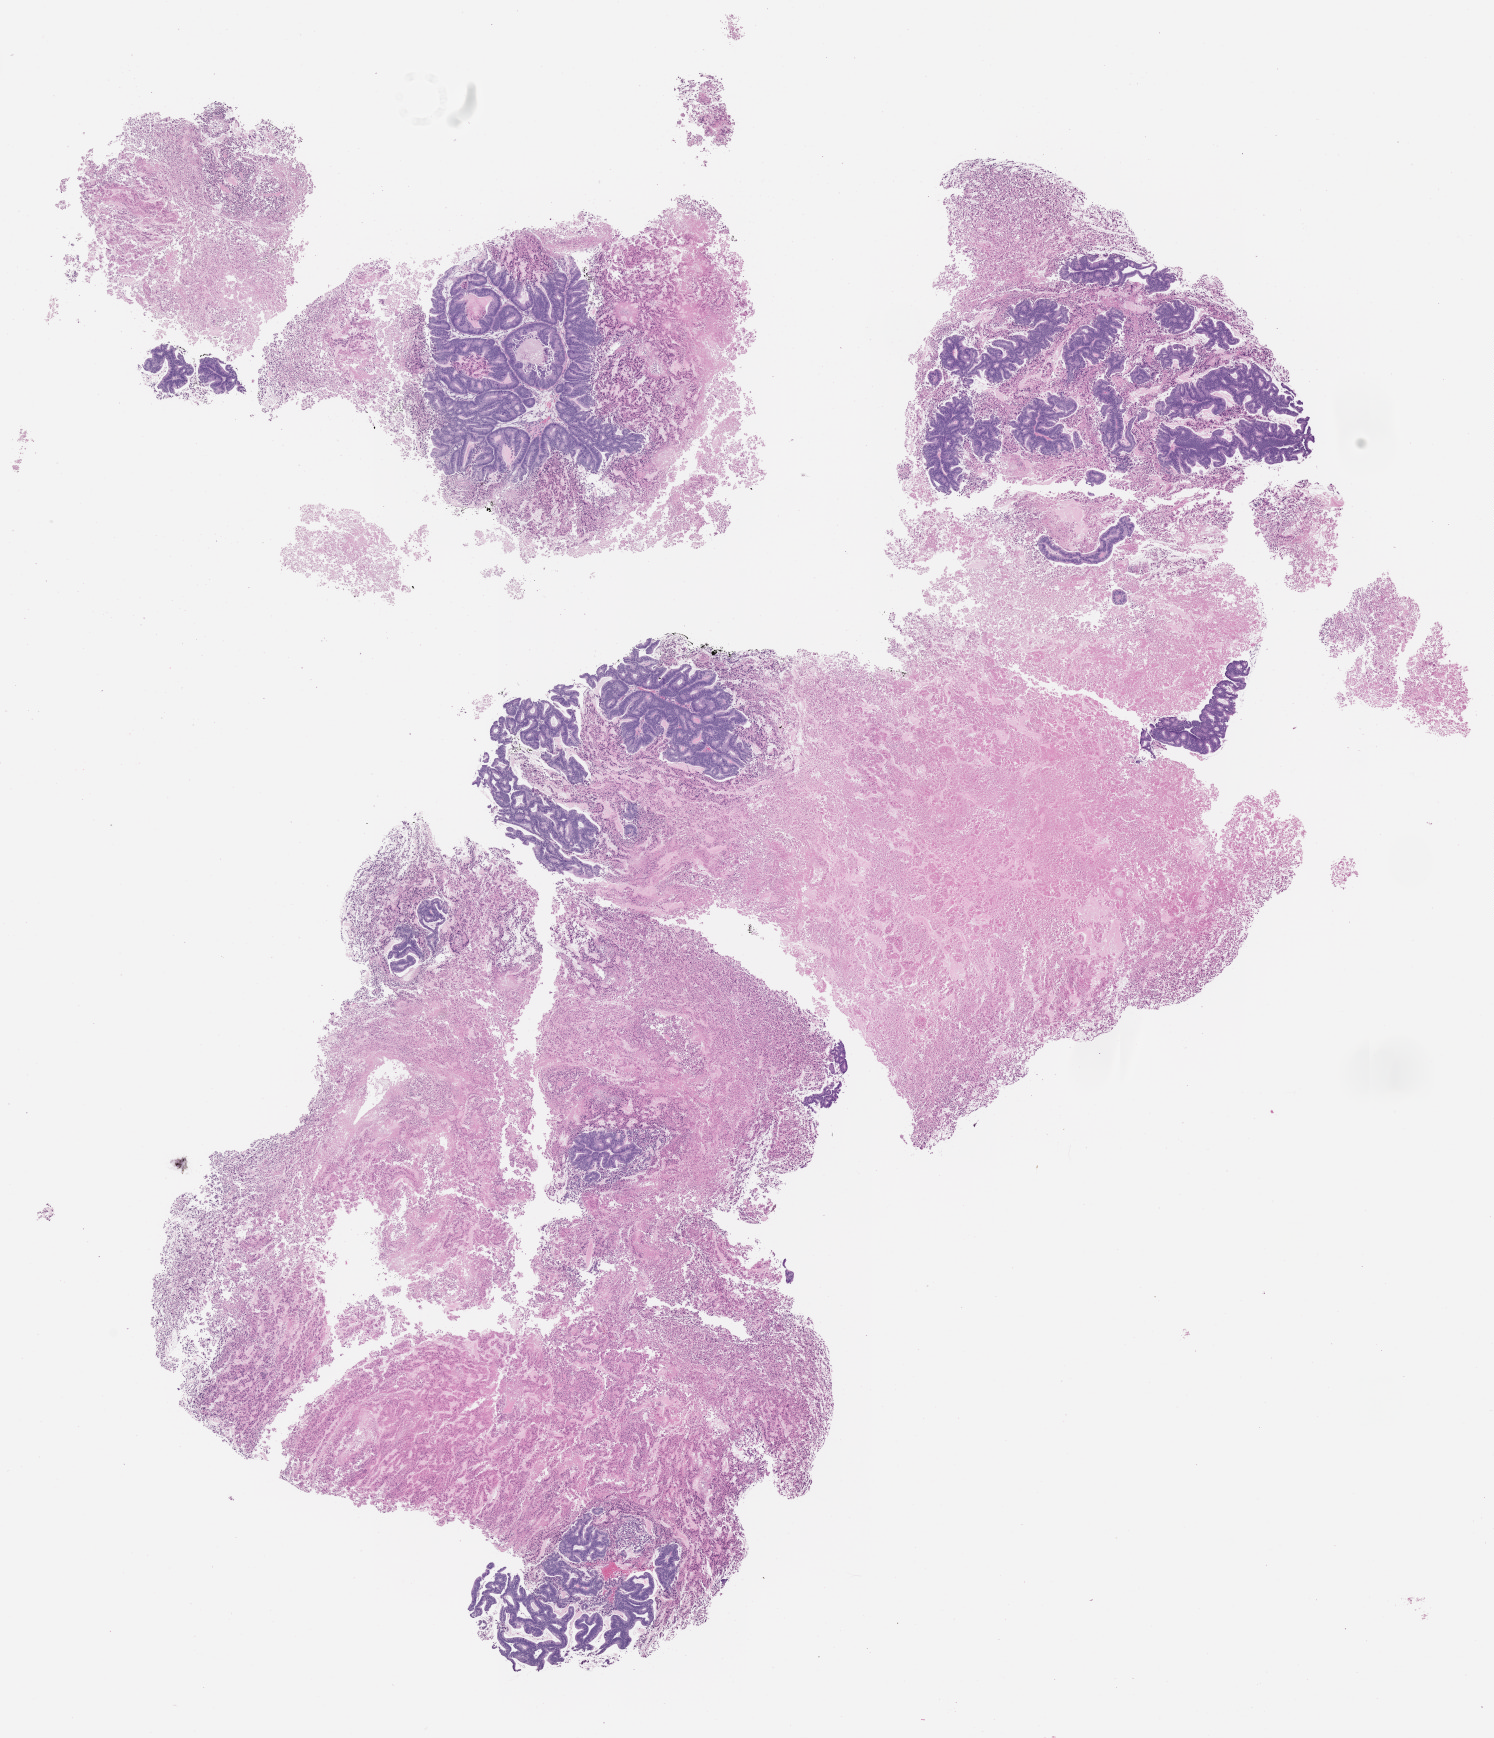
Whole-slide image, hematoxylin and eosin (H&E): patient-derived xenograft (human tumor grown in a mouse), passage 0, shown as a low-resolution overview of the whole scanned area (about 12.0 x 14.0 mm), formalin-fixed, paraffin-embedded (FFPE) tissue, originating tumor site category: colon.
* originating patient diagnosis: Colon Adenocarcinoma